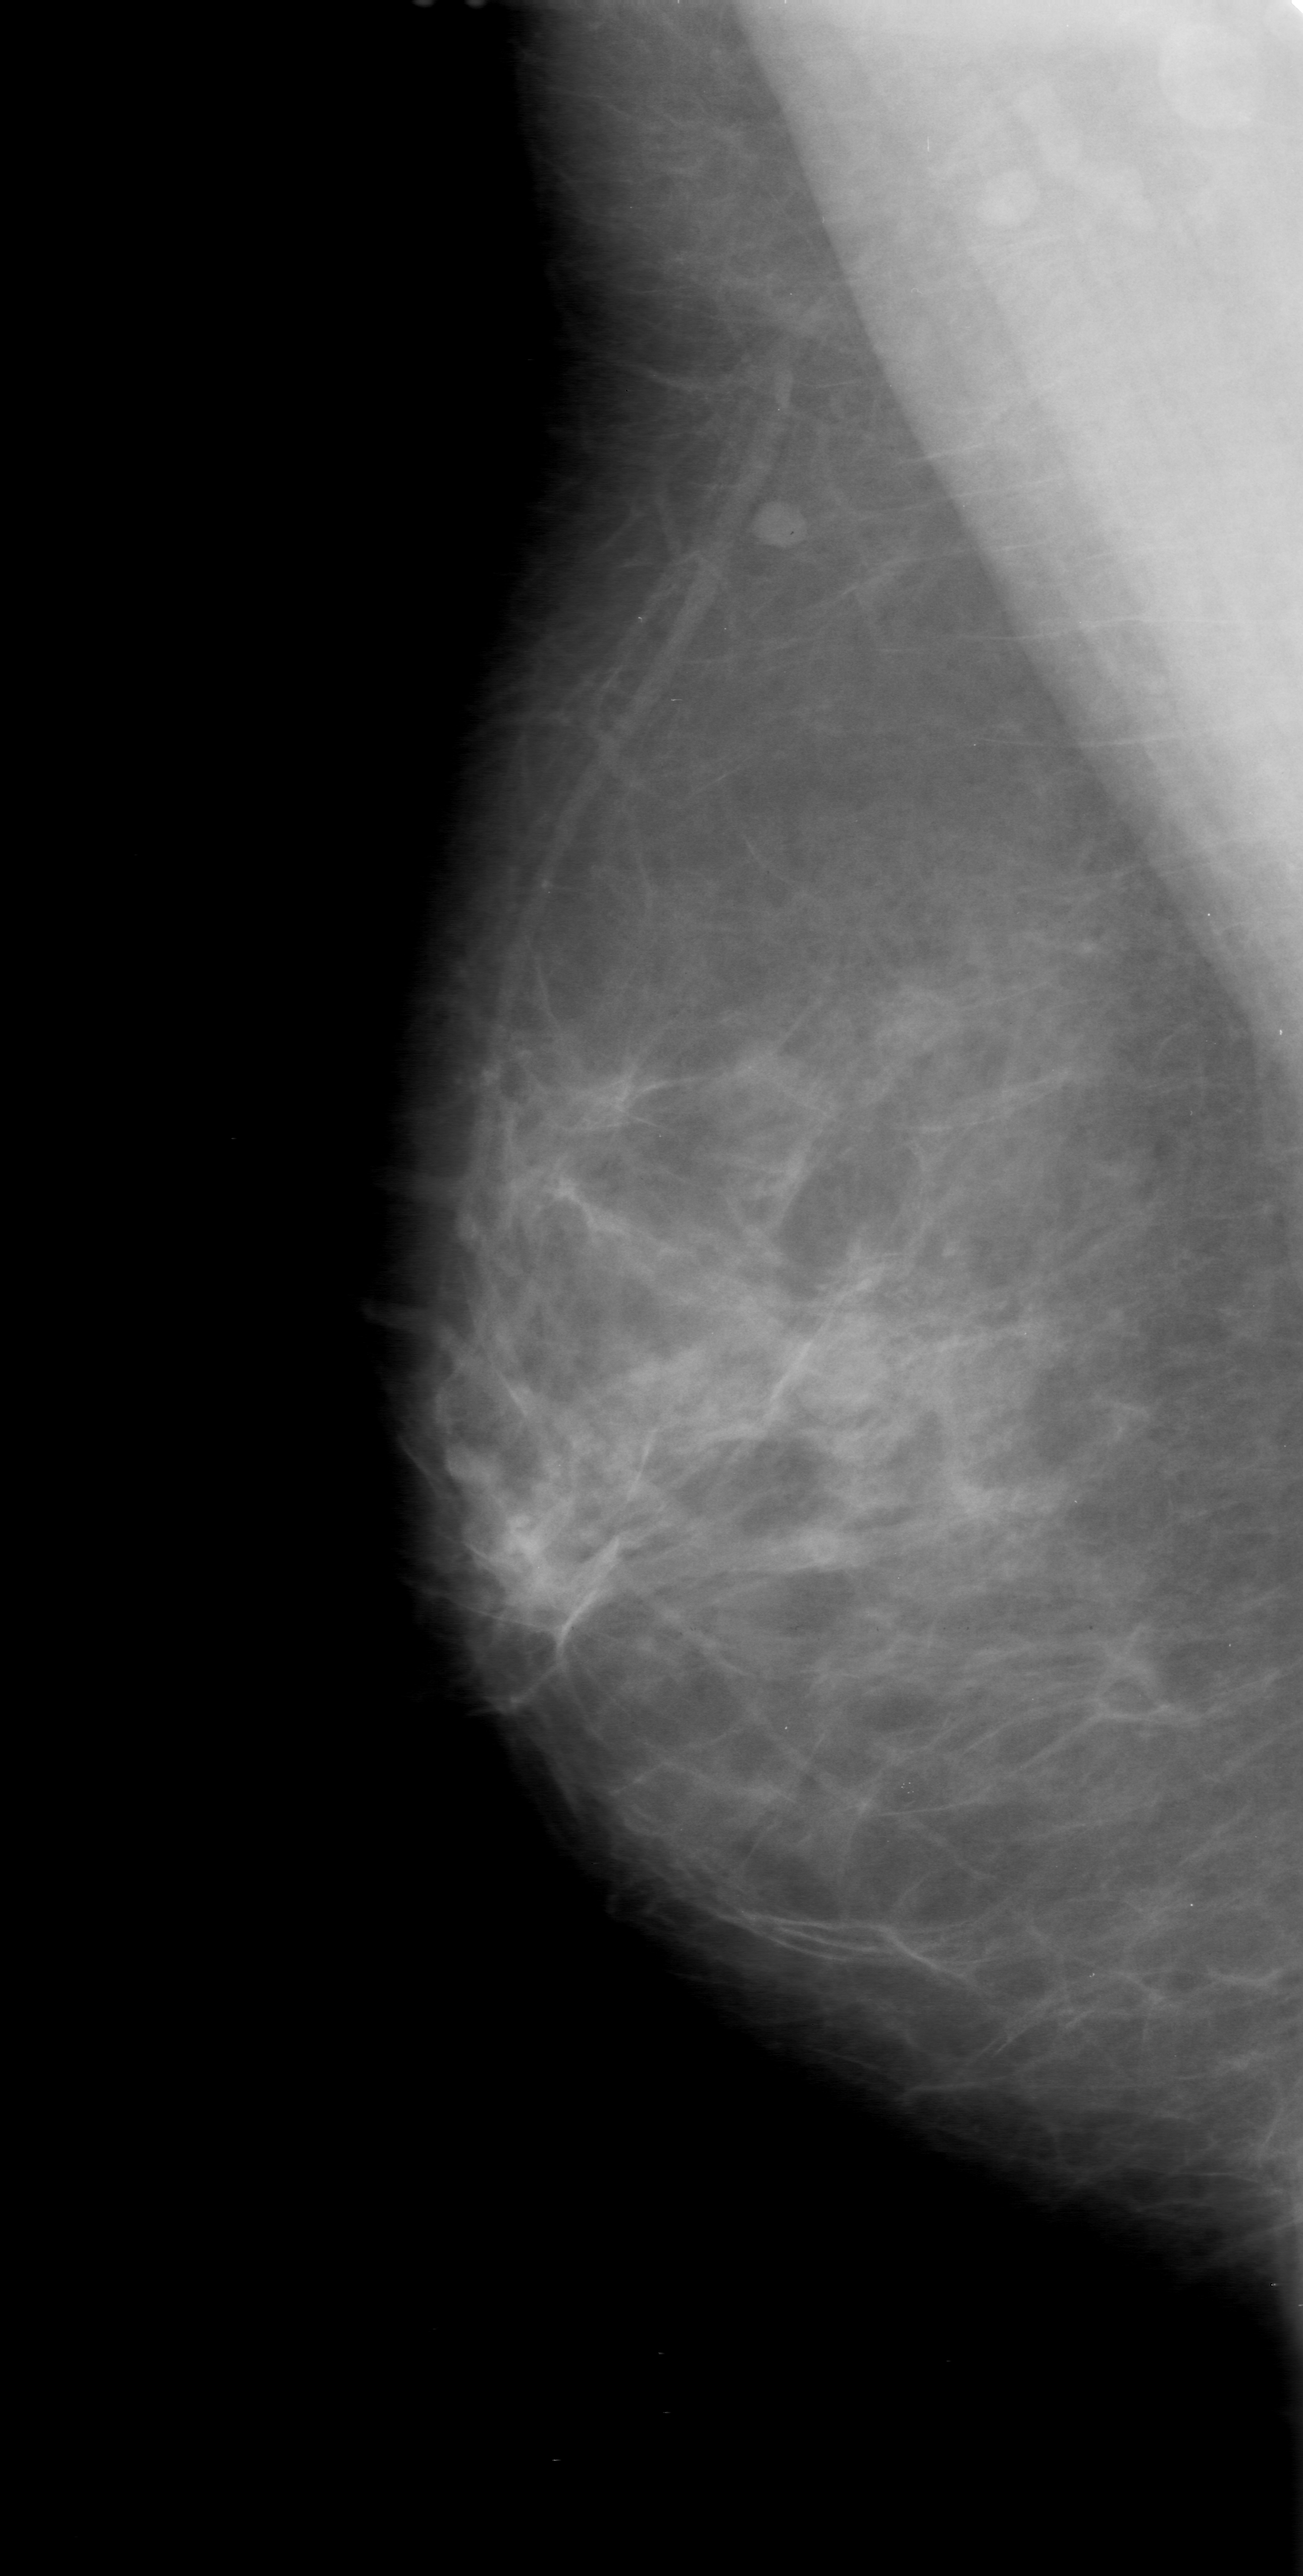
Digitized screen-film mammogram; right breast; MLO view; BI-RADS breast density category 2 (scale 1–4); 1303 × 2576 image matrix.
Marked abnormalities (boxes around the expert regions of interest):
- mass, shape oval, margins obscured; BI-RADS assessment category 0 (incomplete: needs additional imaging); pathology (as recorded): benign: bounding box (x1, y1, x2, y2) in pixels: (717, 1268, 888, 1442)